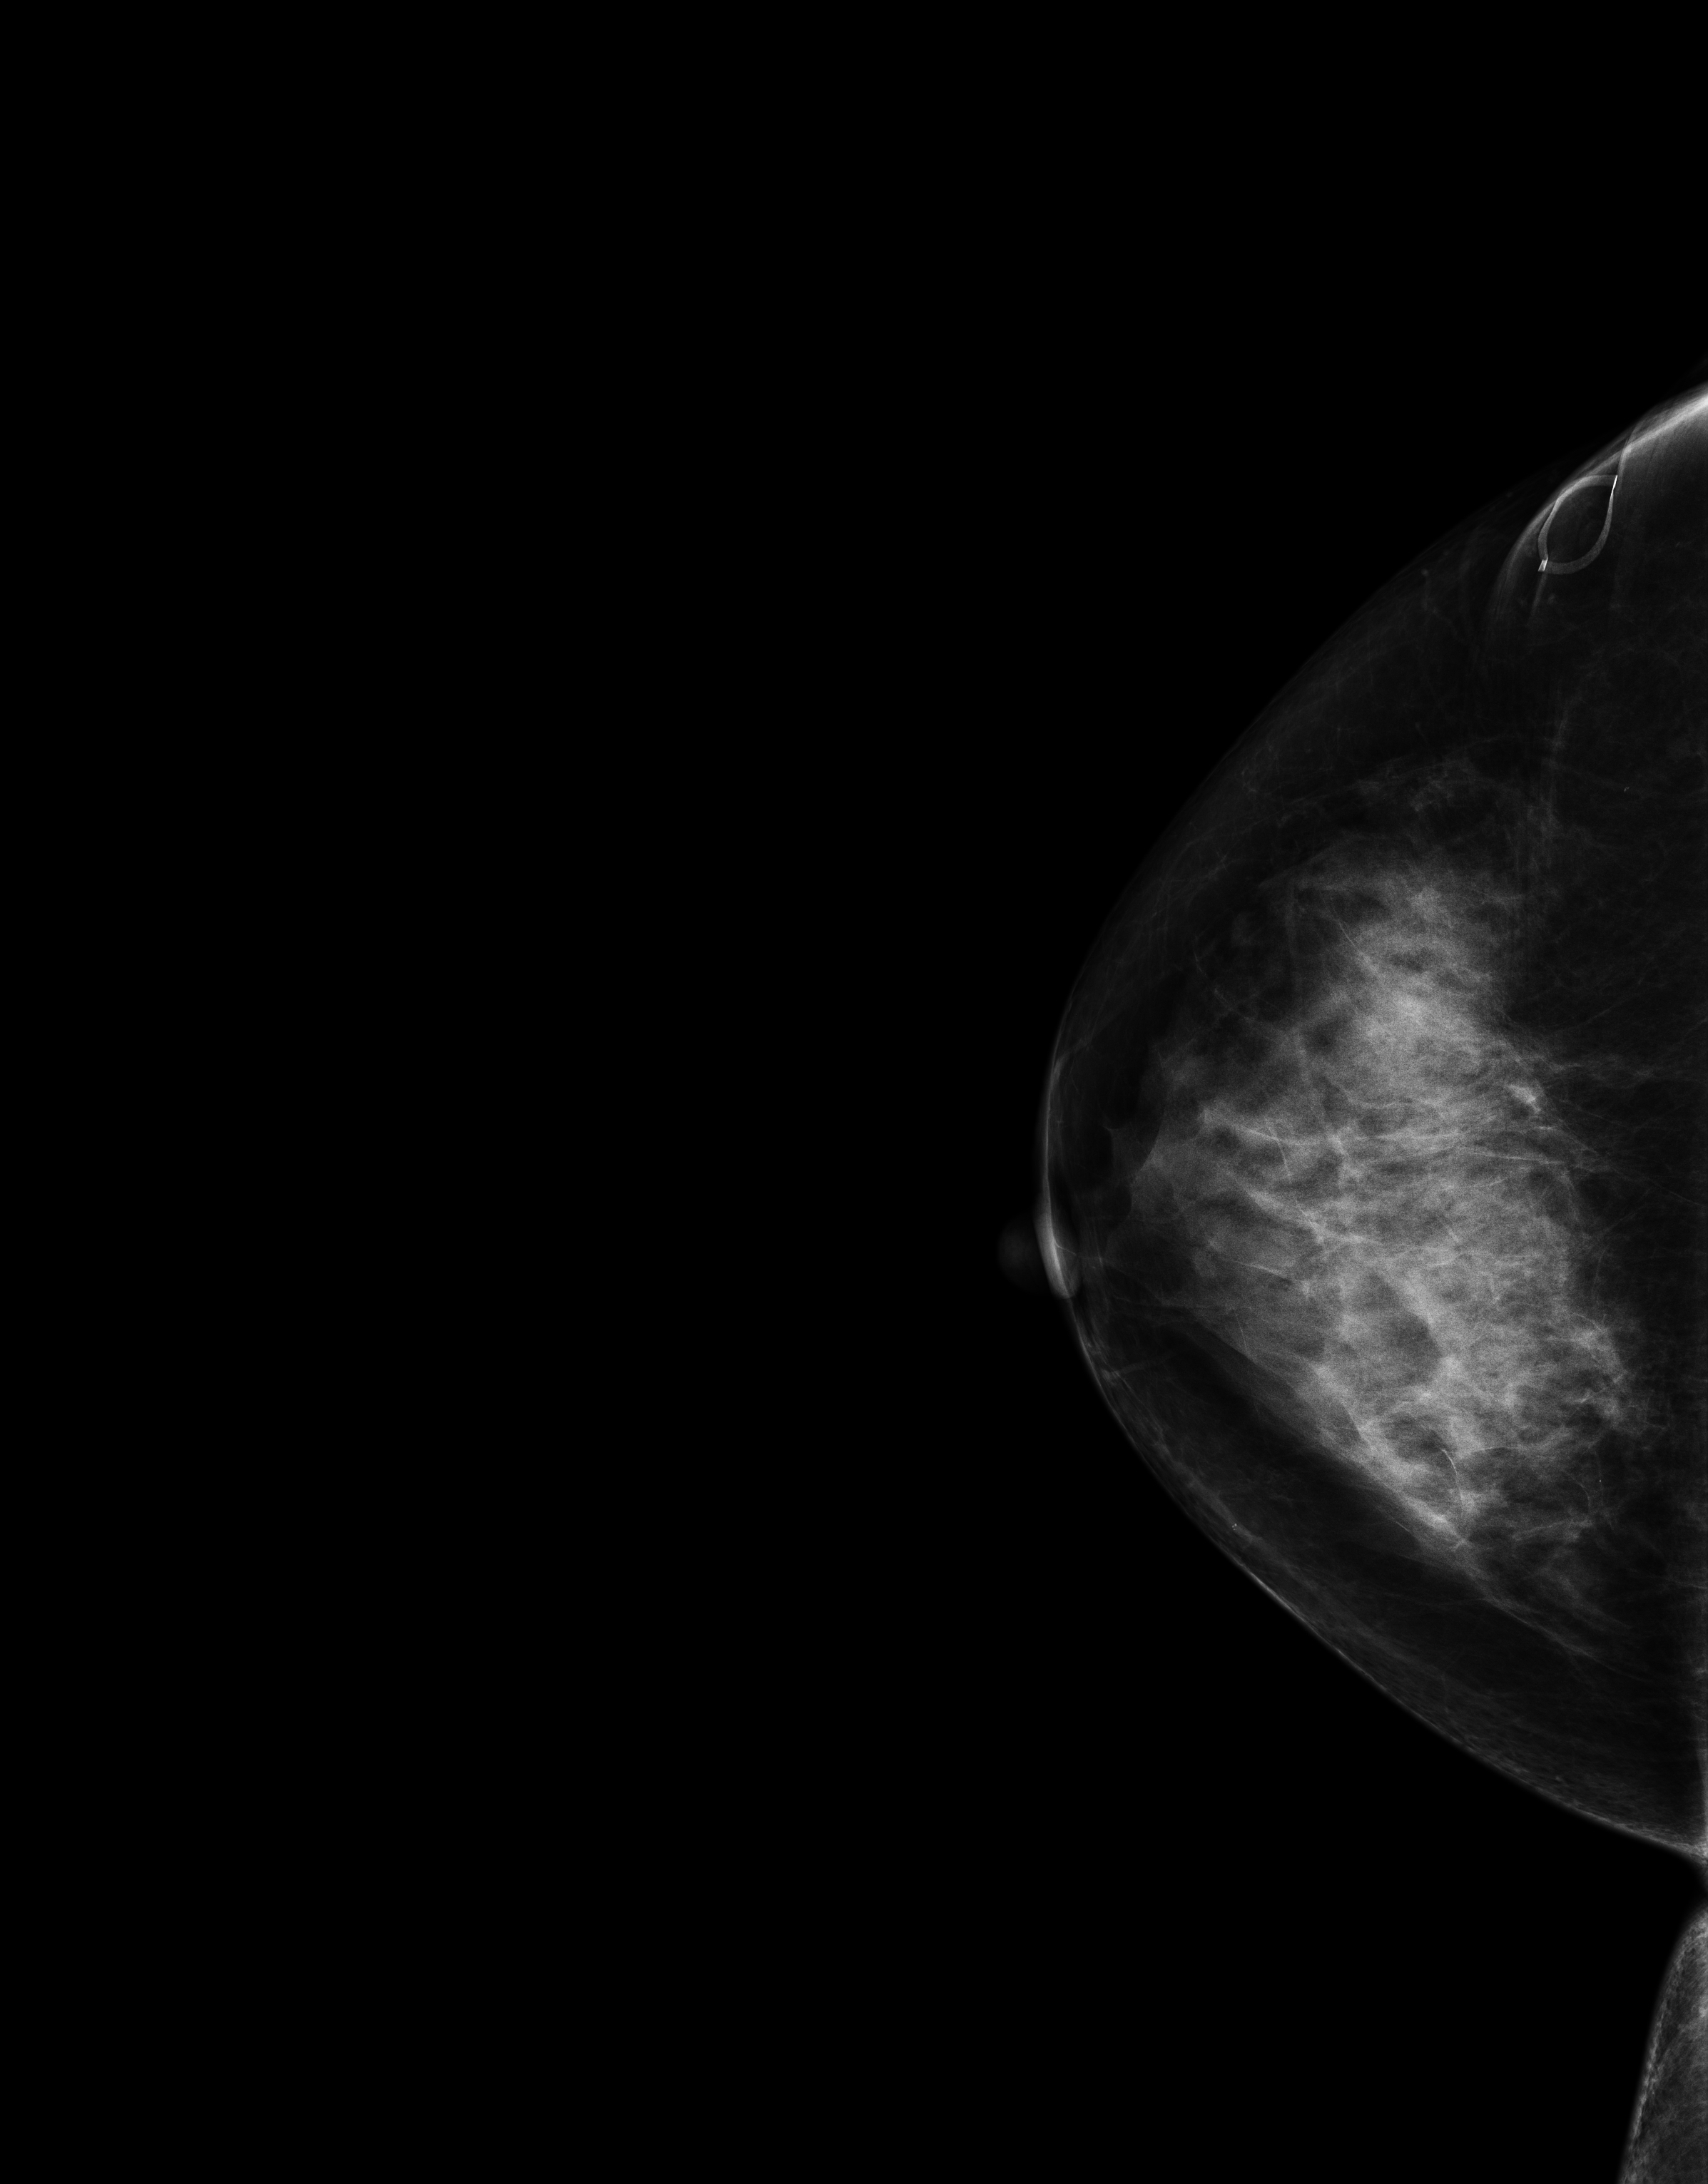
Screening examination, compressed breast thickness 64 mm. Patient: female, 67 years.
Image type: full-field digital mammogram. Breast: right. Projection: CC view.